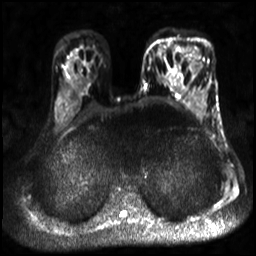
Breast MRI, one axial slice; position 18 of 30 along the scan axis; diffusion-weighted series; image 2 of 4 stored at this slice position (different b-values; order by instance number); 3 T; 4 mm slice thickness; 256 × 256 image matrix, field of view 320 × 320 mm. Female patient.
Outlined on this slice (manually delineated by an expert):
- tumour on diffusion-weighted imaging: box from (x=189, y=51) to (x=203, y=73) px